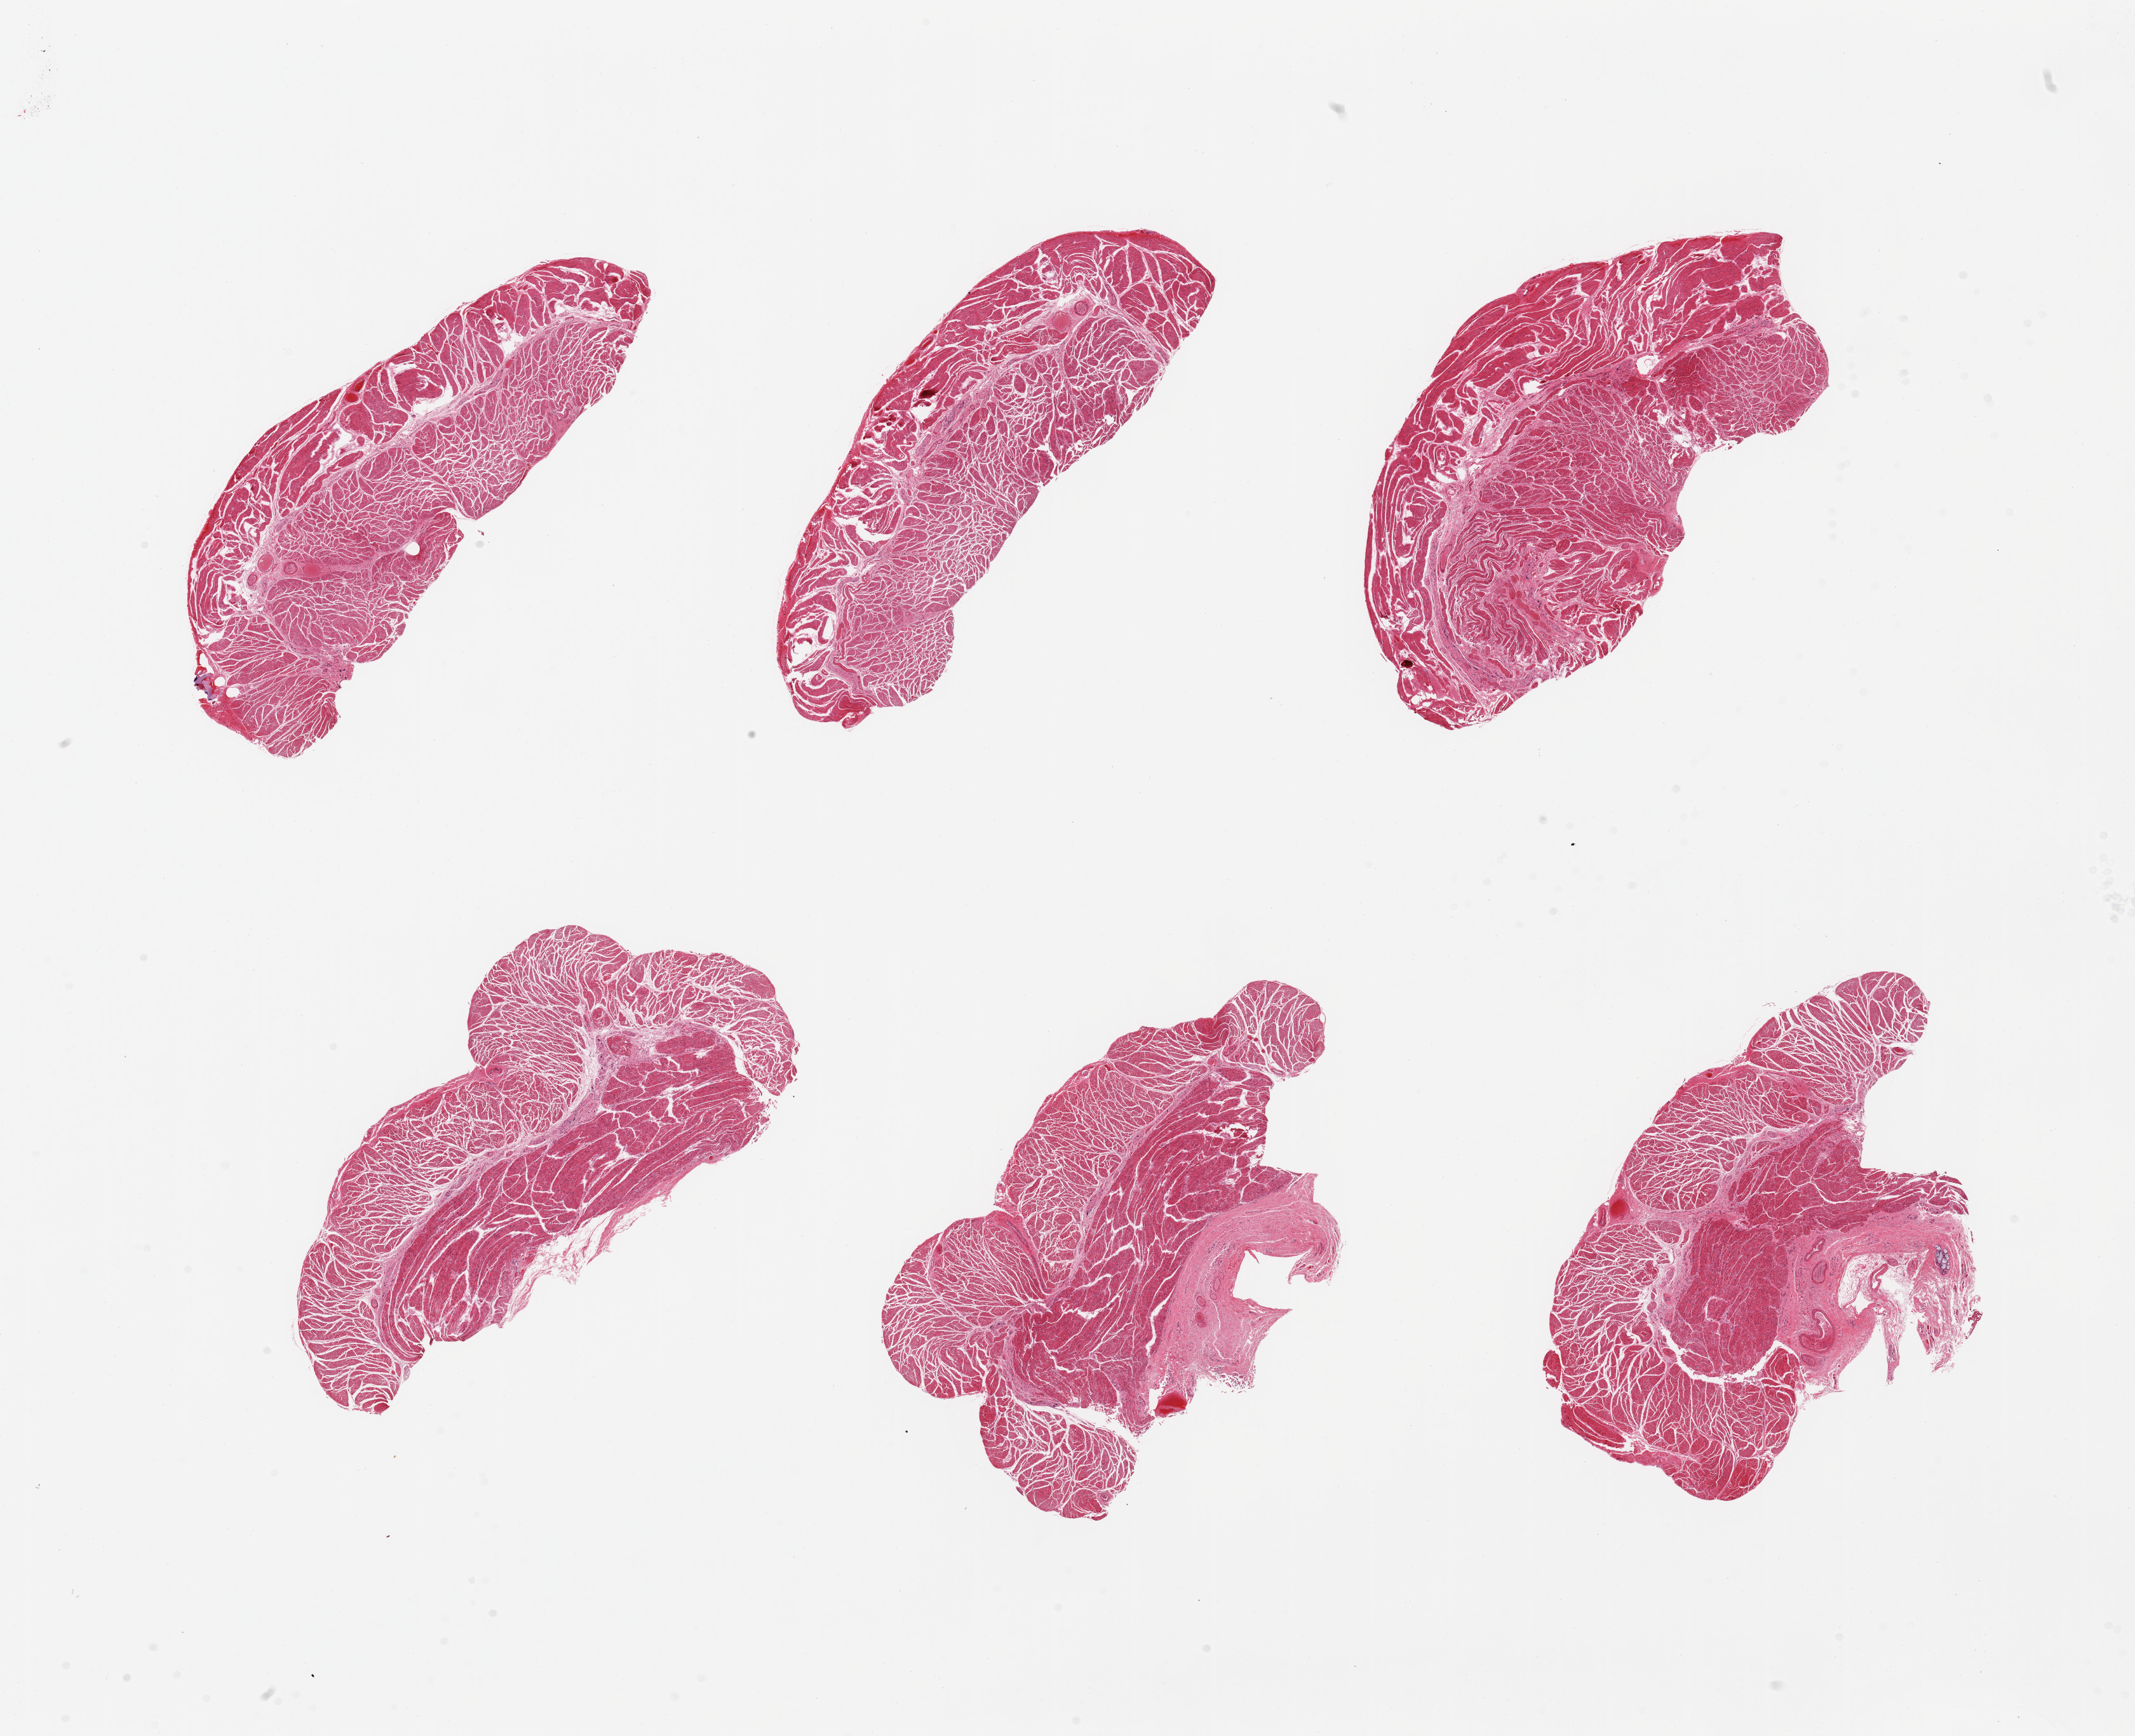
Digitized haematoxylin and eosin-stained section, brightfield — low-resolution overview of the scanned area, about 26.6 x 21.6 mm. PAXgene-fixed paraffin-embedded (PFPE) section. Section of esophageal muscle (target tissue). Tissue donor sample. Male donor.
- review note (as recorded): 6 pieces; well trimmed except for small submucosal gland